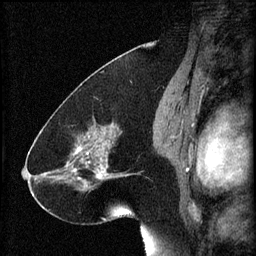
Breast MRI (dynamic contrast-enhanced), one sagittal slice; slice 36 of 60 in the series (ordered by position); 3 images stored at this slice position (order not interpretable as contrast timing); 1.5 T; TE 4.2 ms, TR 8.2 ms; 256 × 256 image matrix, field of view 180 × 180 mm. Female patient, age 41 years.
Outlined on this slice (semi-automatic segmentation, software-assisted and operator-edited):
- analysis volume of interest (the breast-tissue region the enhancement analysis was run in; not a lesion): bounding box <72,120,134,193> (left, top, right, bottom; pixels)
- tumour enhancement mask (voxels above the 70 % enhancement threshold inside the analysis volume of interest): <72,124,129,187>